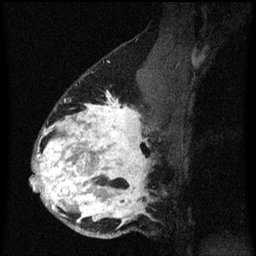
Breast MRI (dynamic contrast-enhanced), one sagittal slice; dynamic contrast-enhanced series, image 2 of 3 at this slice position (ordered by acquisition); 1.5 T; TE 4.2 ms, TR 8.4 ms; 2 mm slice thickness; 256 × 256 image matrix, field of view 180 × 180 mm. Female patient, age 34 years. From the clinical record (not read from this slice): setting: breast cancer imaged before/during neoadjuvant chemotherapy; receptor status: HR-positive, HER2-negative.
Annotated regions visible in this slice (semi-automatic segmentation, software-assisted and operator-edited):
- analysis volume of interest (the breast-tissue region the enhancement analysis was run in; not a lesion): box from (x=30, y=58) to (x=169, y=239) px
- tumour enhancement mask (voxels above the 70 % enhancement threshold inside the analysis volume of interest): (x=32, y=94)–(x=151, y=227)